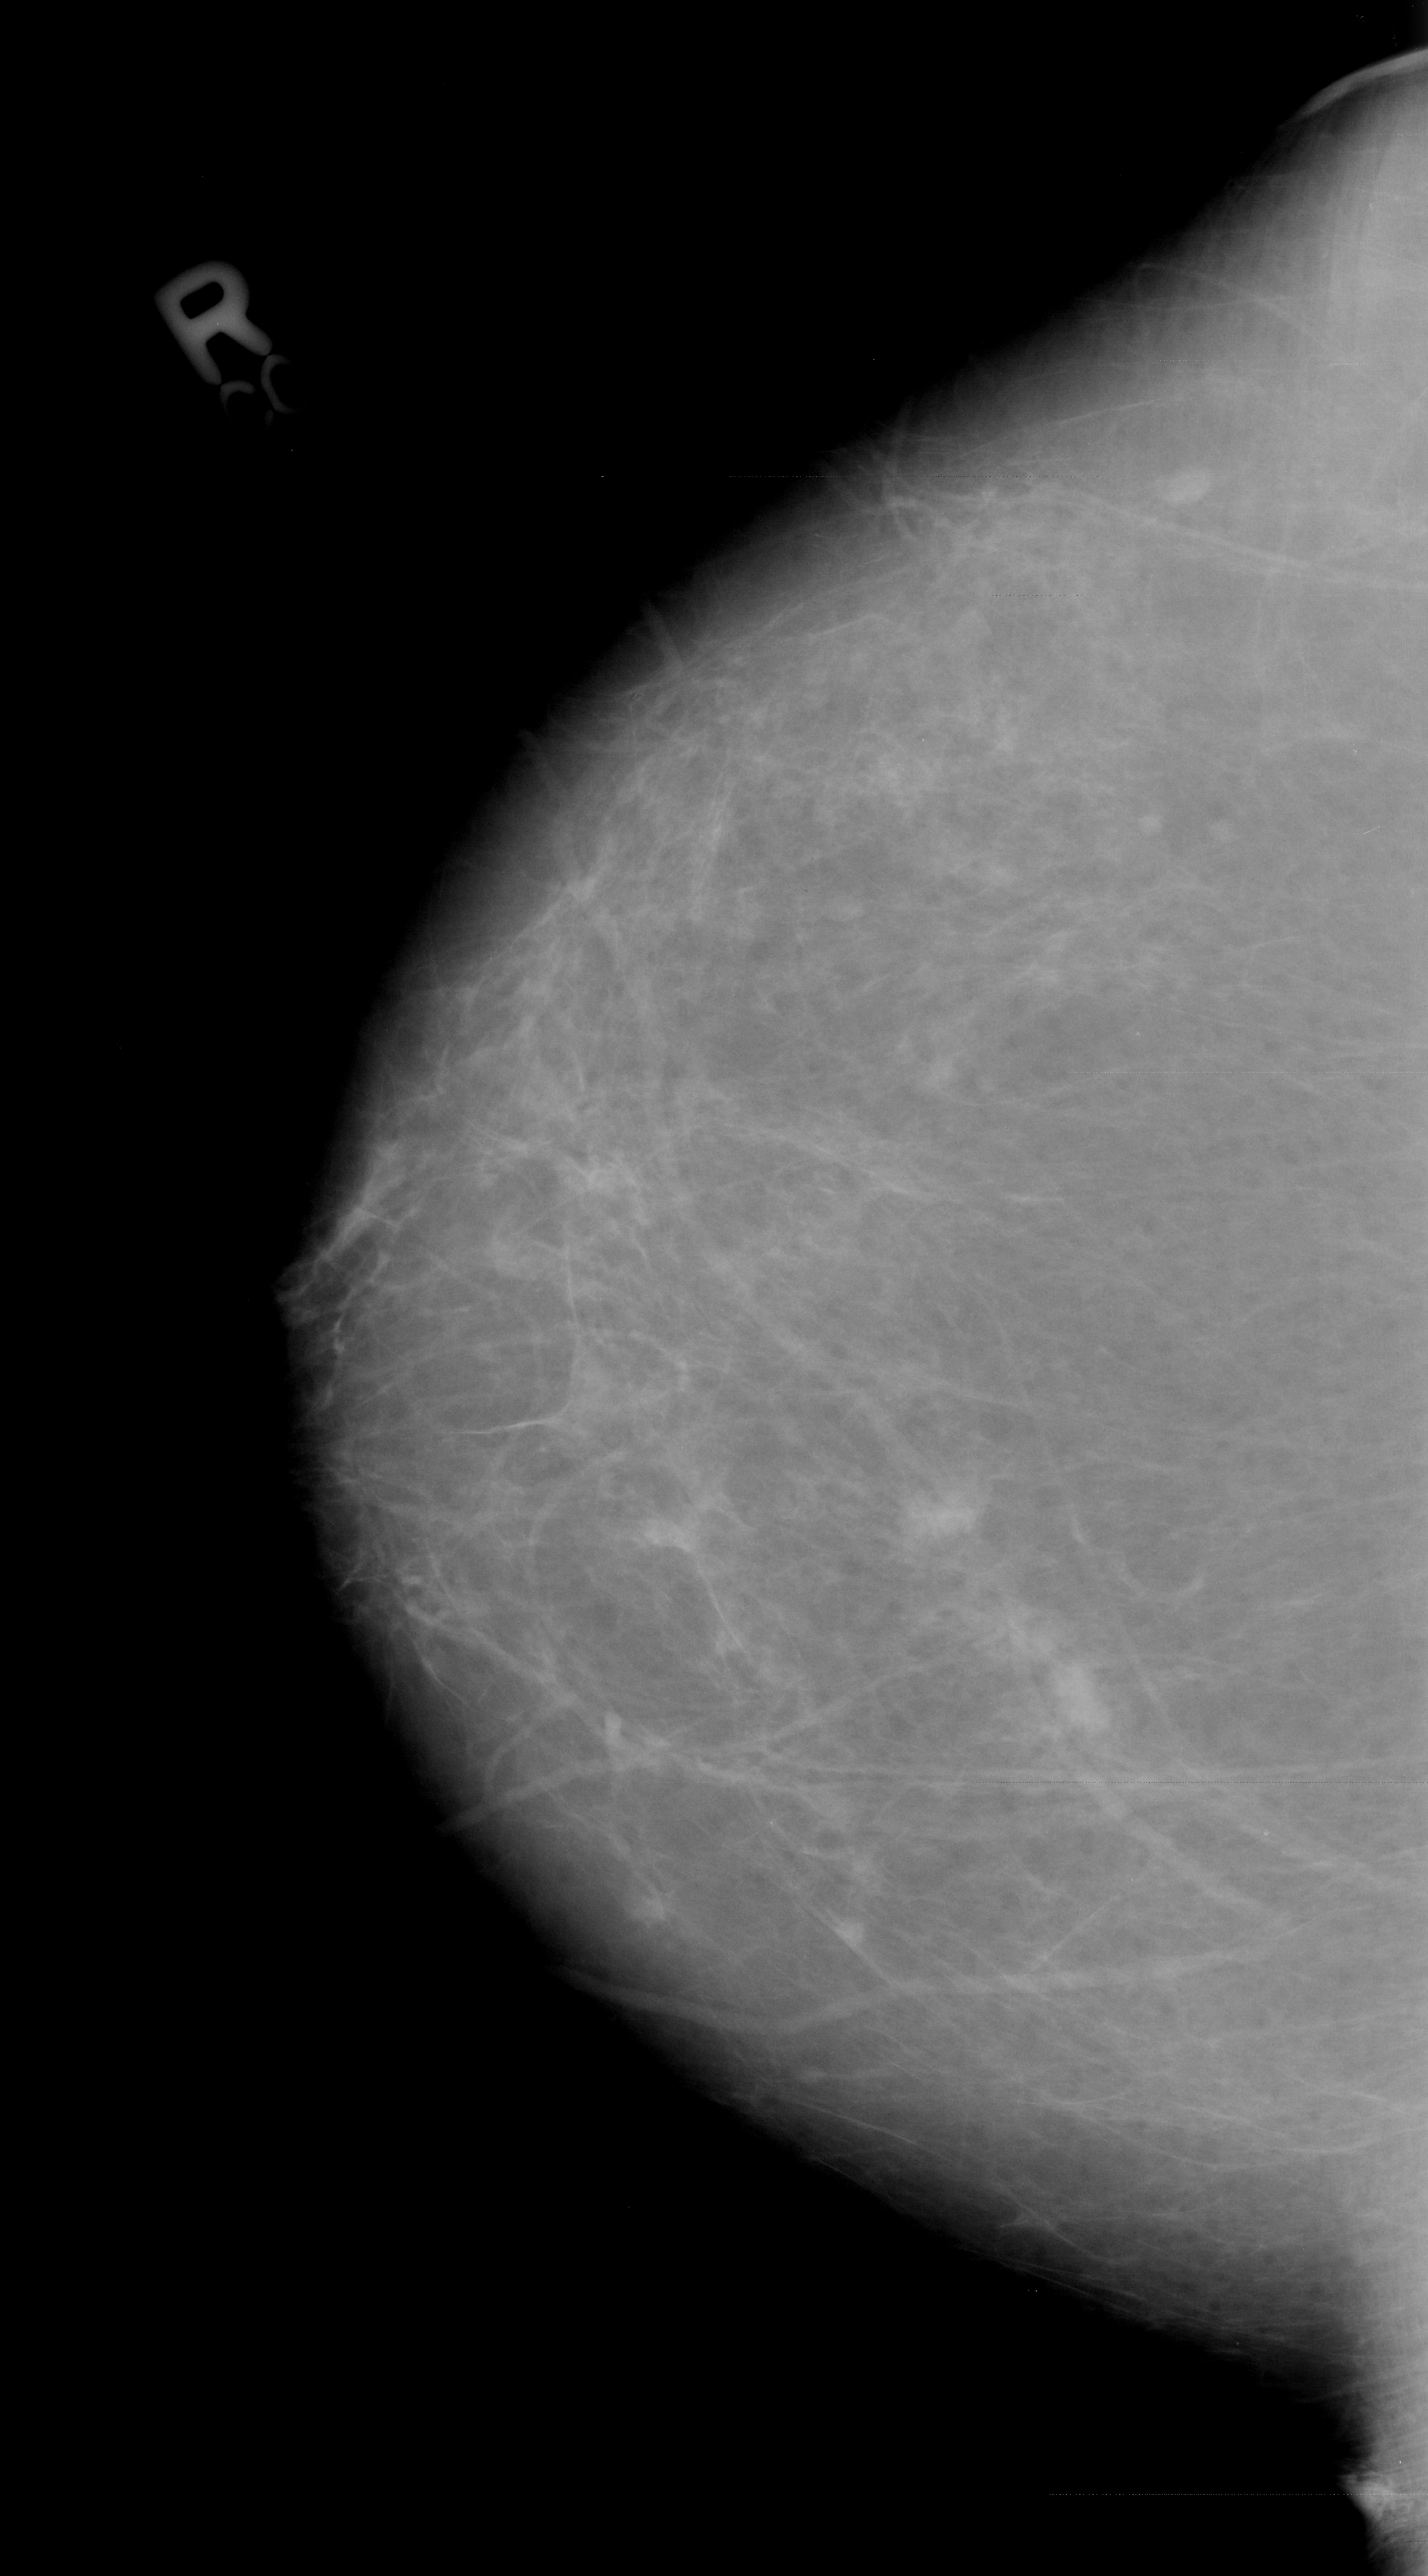
Scanned film-screen mammogram; right breast; CC view; BI-RADS breast density category 1 (scale 1–4).
Radiologist-marked abnormalities on this image: Finding 1 of 2: mass, shape irregular, margins ill defined; BI-RADS assessment category 4; subtlety rating 3 on a 1 (subtle) to 5 (obvious) scale; pathology result (as recorded, not read from the image): malignant. Finding 2 of 2: mass, shape irregular, margins ill defined; BI-RADS assessment category 4; subtlety rating 3 on a 1 (subtle) to 5 (obvious) scale; pathology (as recorded): malignant.